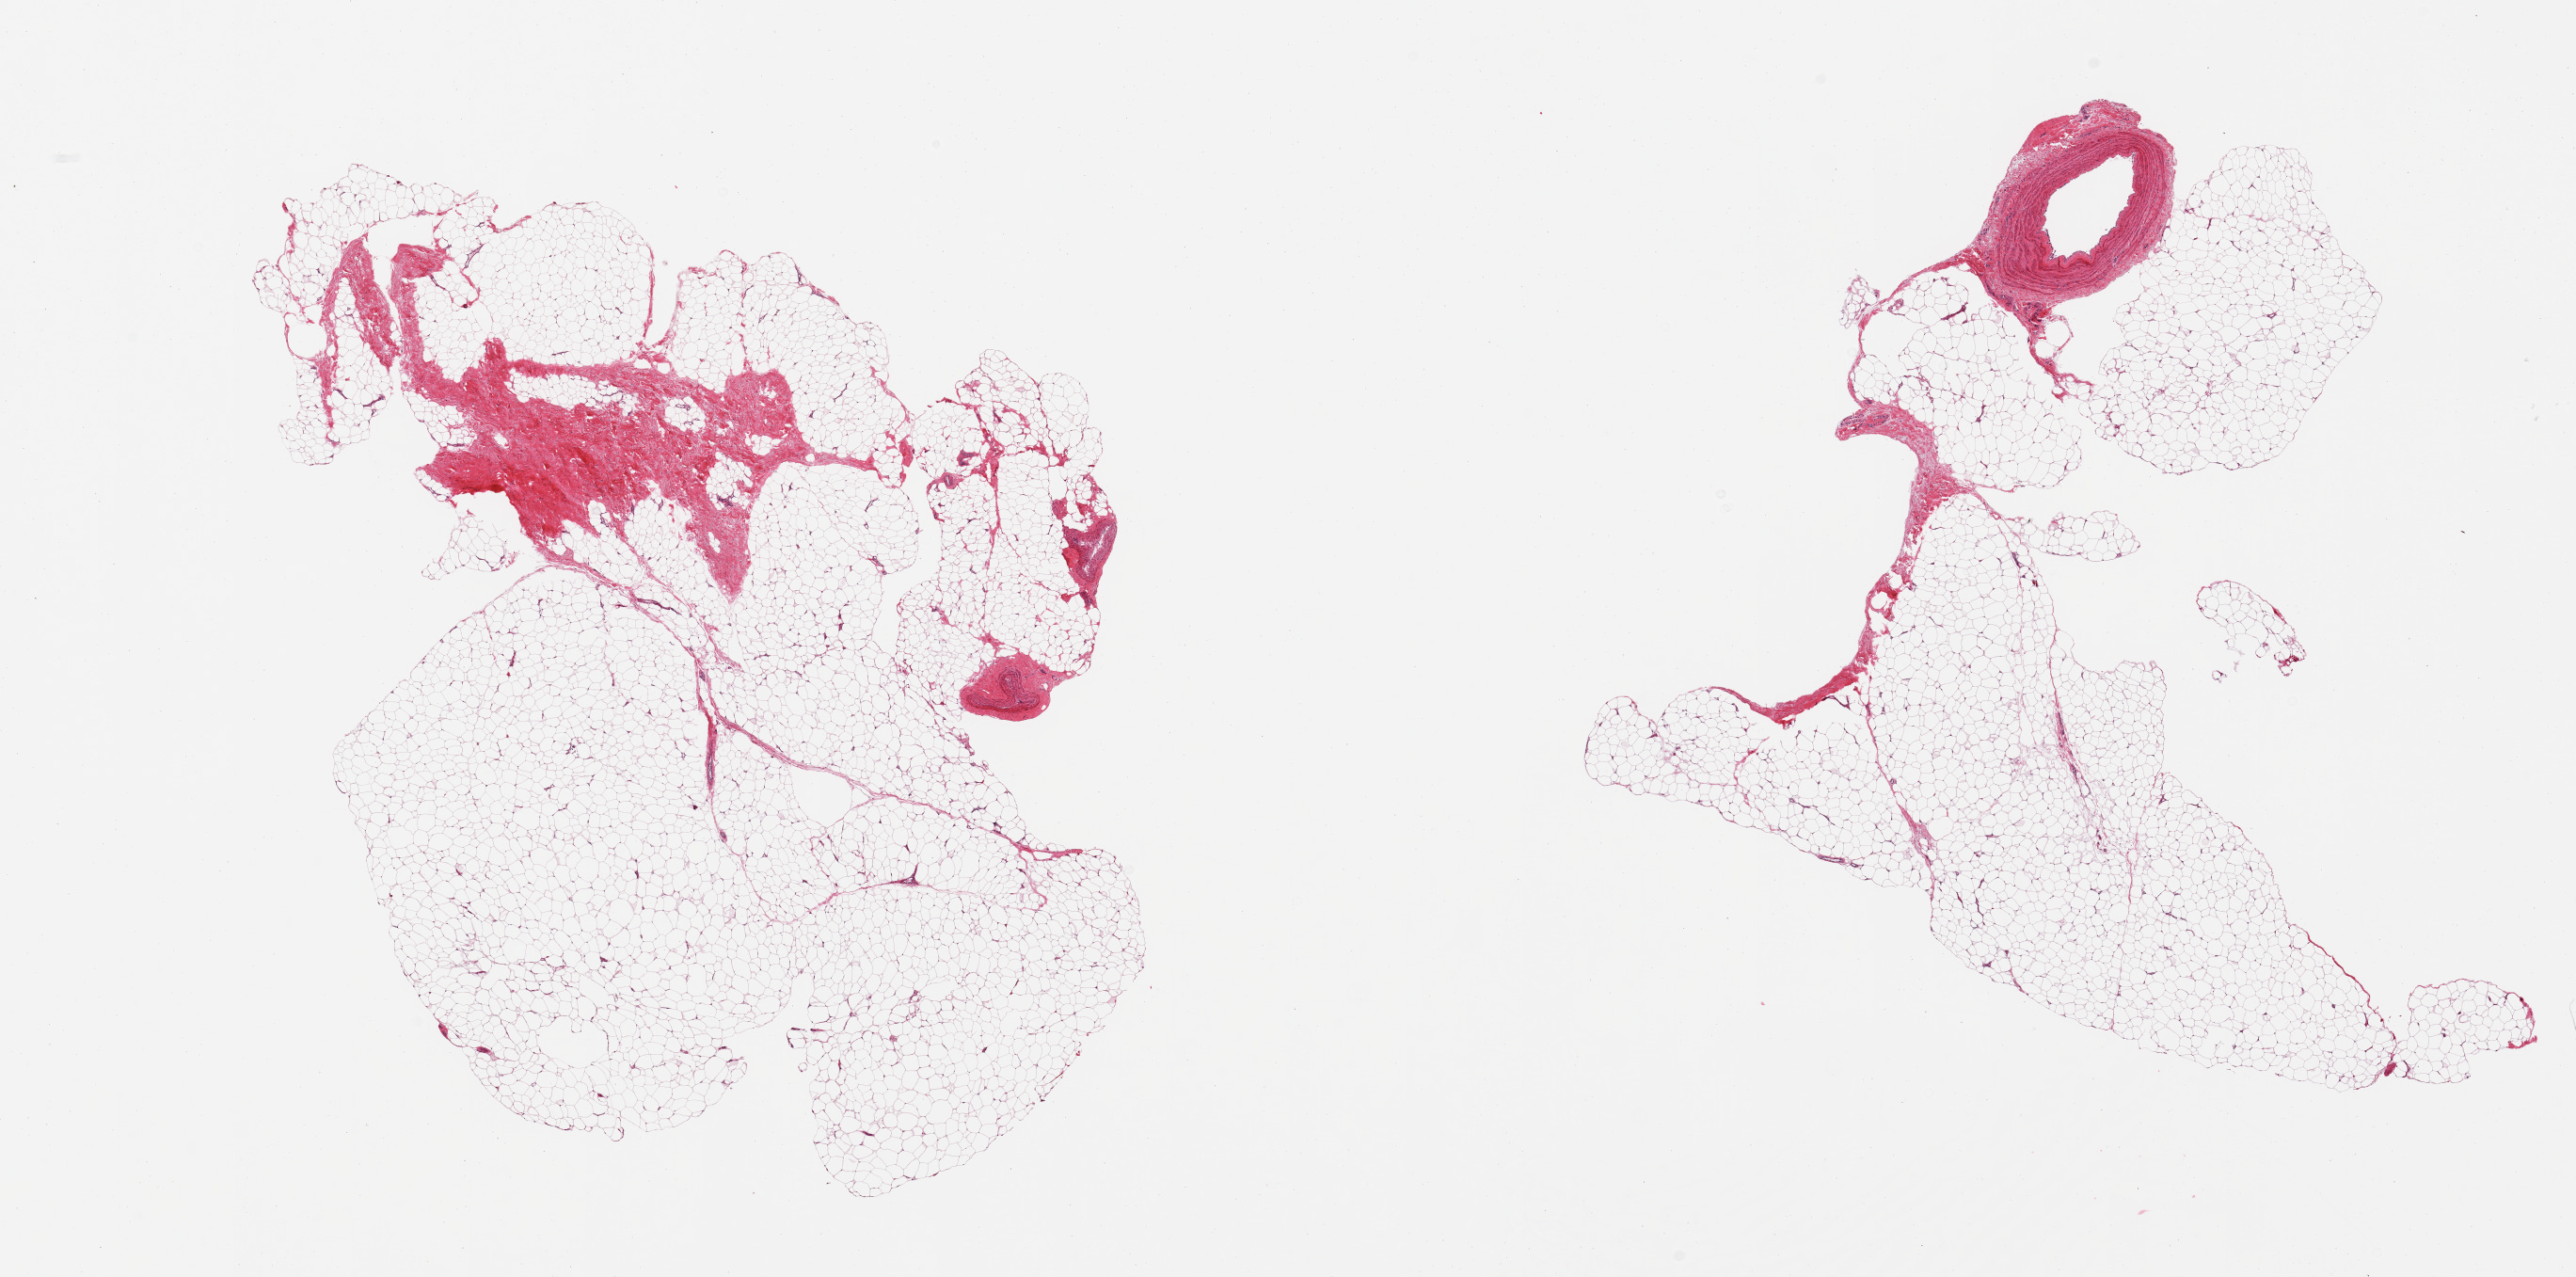
Whole-slide image, H&E stain, brightfield, whole scanned area (about 21.7 x 10.7 mm) shown as a low-resolution overview, PAXgene-fixed, paraffin-embedded tissue, target tissue: adipose tissue, tissue donor sample. Male donor.
Pathologist's review note for this sample: 2 pieces, fascia/vascular elements (including muscular arteriole, ~1mm) are ~15-20% tissue.